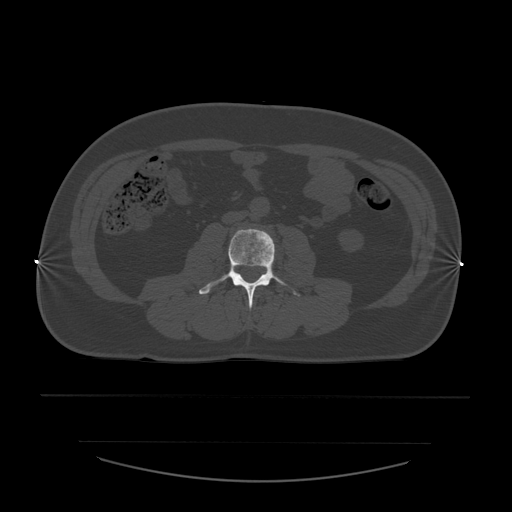
CT including the spine, one axial slice; slice 173 of 532 in the series (ordered by position); reconstruction kernel STANDARD; 120 kVp; bone window (W 1800 / L 400 HU); 1.25 mm slice thickness; 512 × 512 image matrix. Patient age 44 years. From the clinical record (not read from this slice): primary cancer: soft tissue sarcoma.
Annotated regions visible in this slice (semi-automatic segmentation, software-assisted and operator-edited):
- L3 vertebra: bounding box (x1, y1, x2, y2) in pixels: (199, 229, 301, 309)